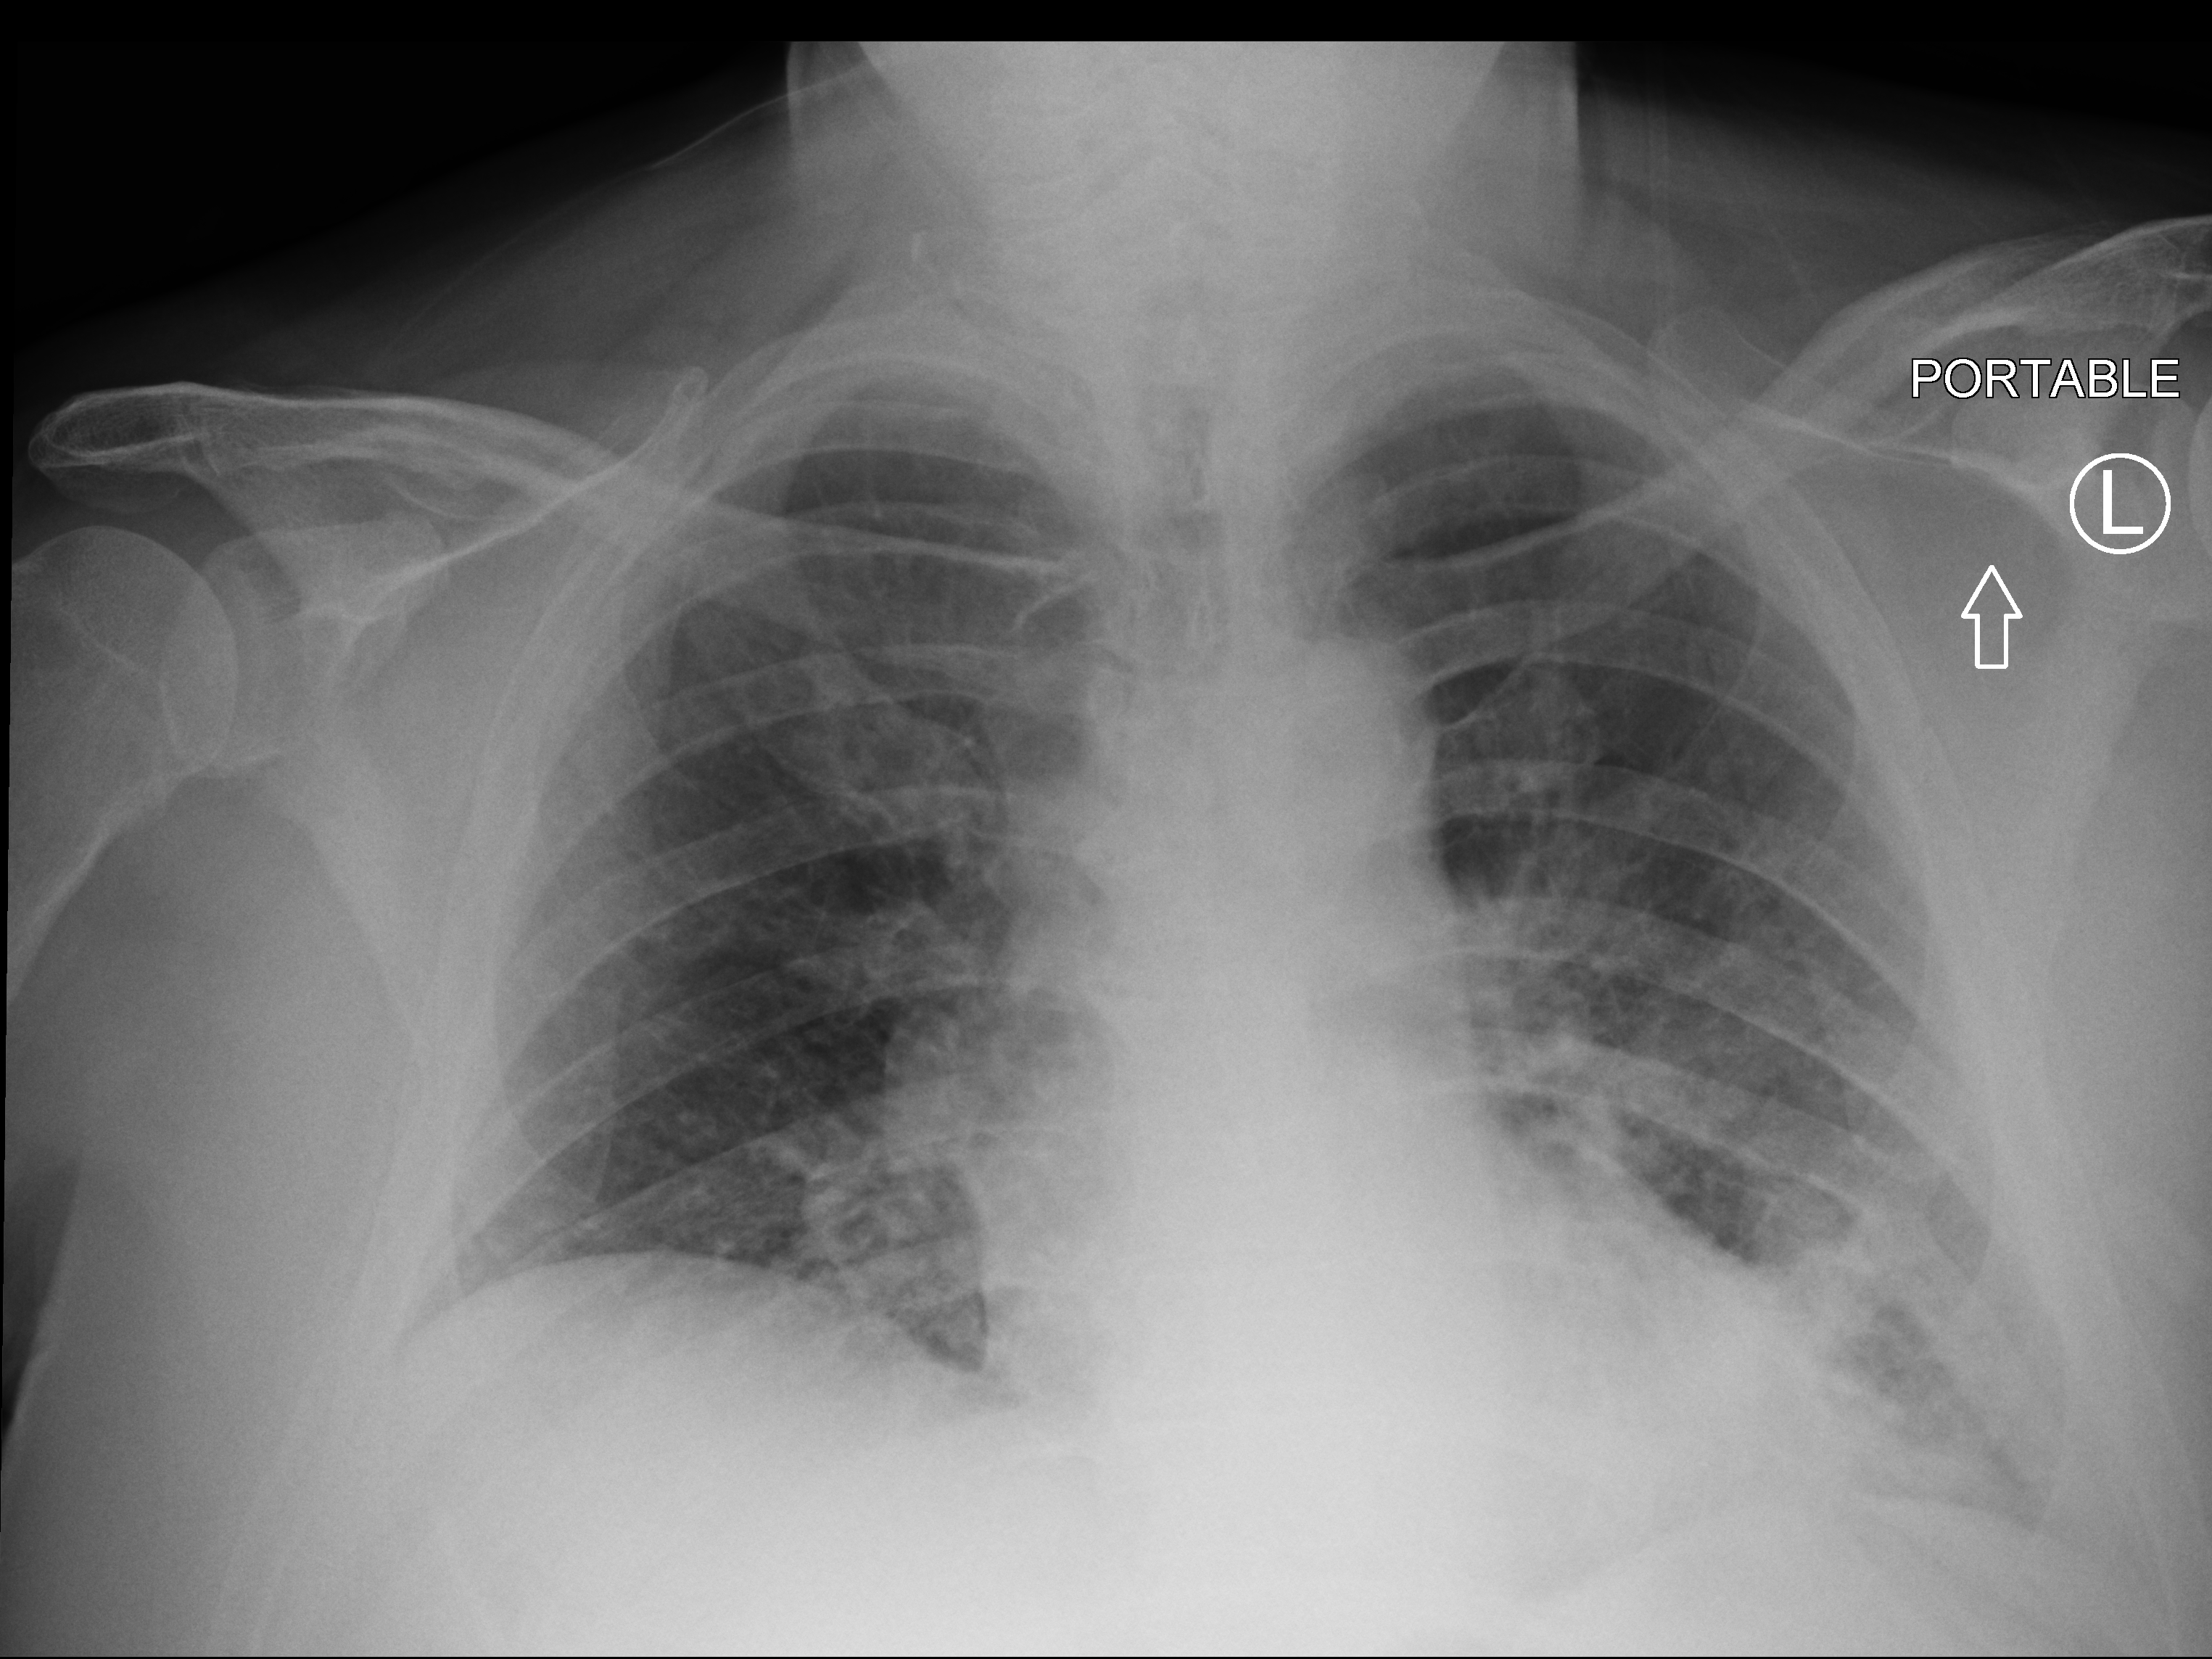
Bedside chest radiograph (computed radiography), anteroposterior (AP) projection. Male patient hospitalised with COVID-19, age 60–74 years.
From the hospital-stay record, not from the radiograph (when in the stay this image was taken is not recorded): mechanically ventilated during this hospital stay: no.